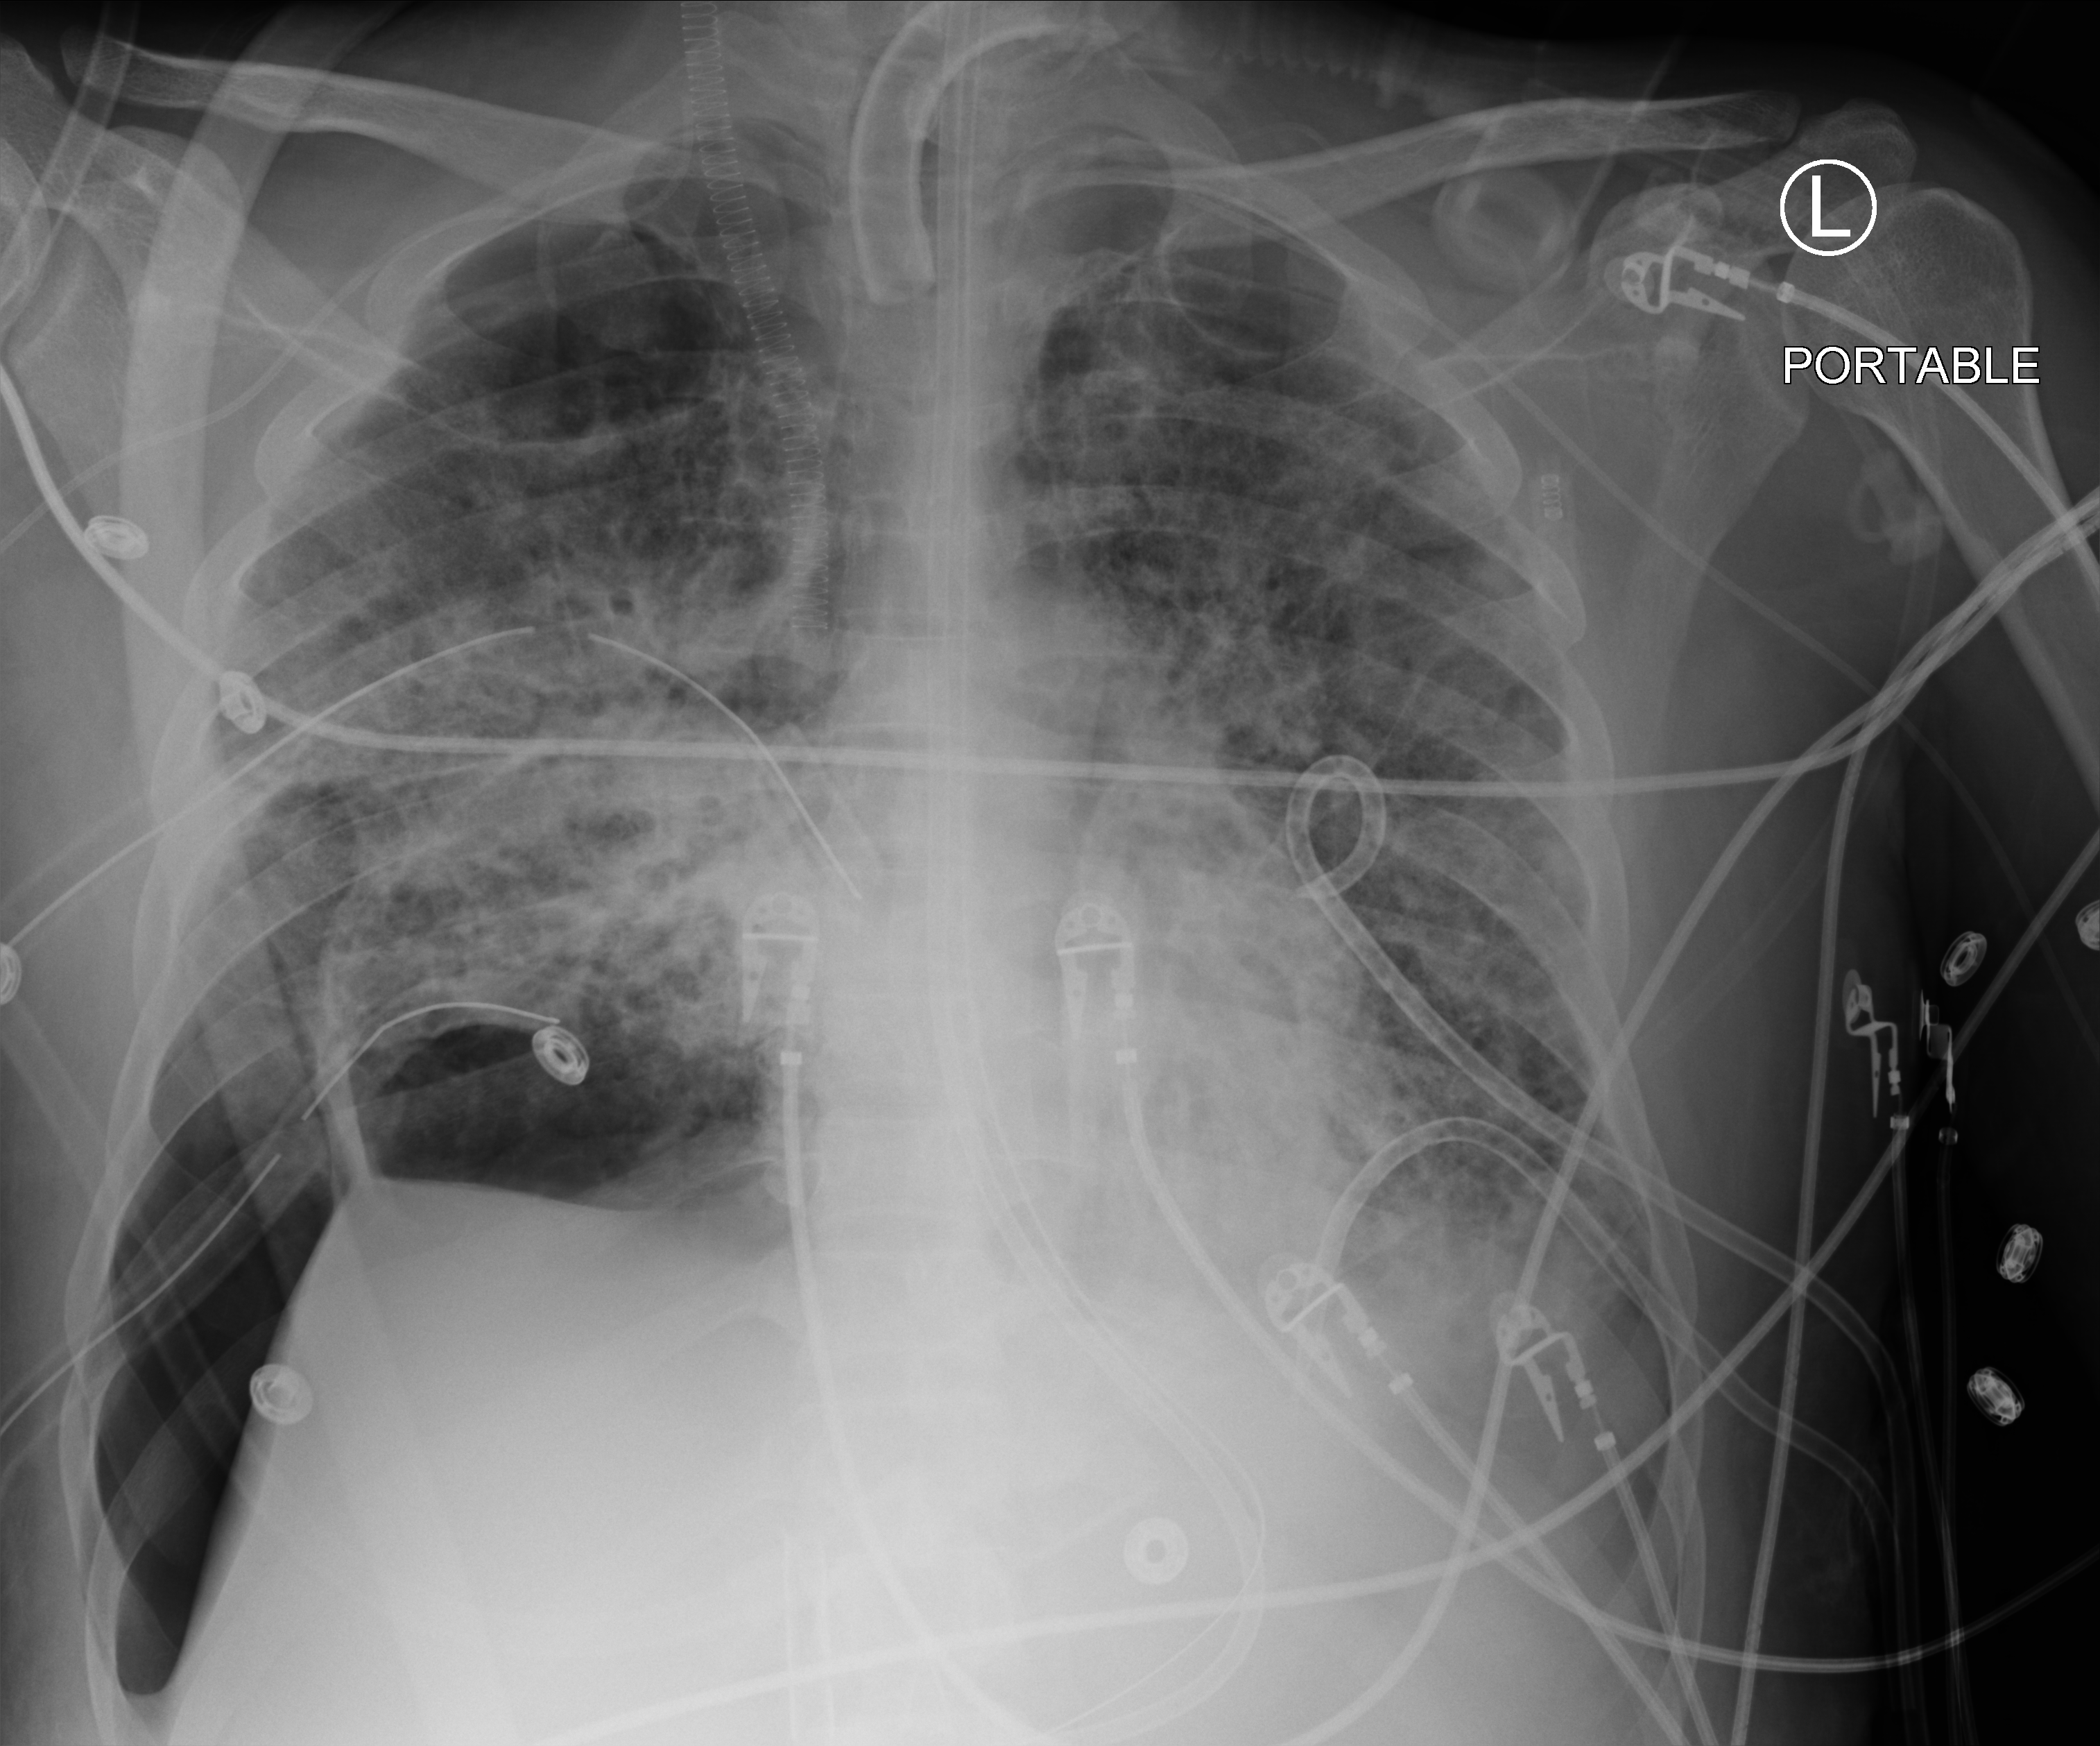
Portable chest radiograph. Patient hospitalised with COVID-19, aged 18–59 years.
Admission-level facts for this patient (not findings on this image; timing relative to this image not recorded):
- mechanically ventilated during this hospital stay: yes
- hypertension (admission record): no
- admitted to intensive care during this hospital stay: yes